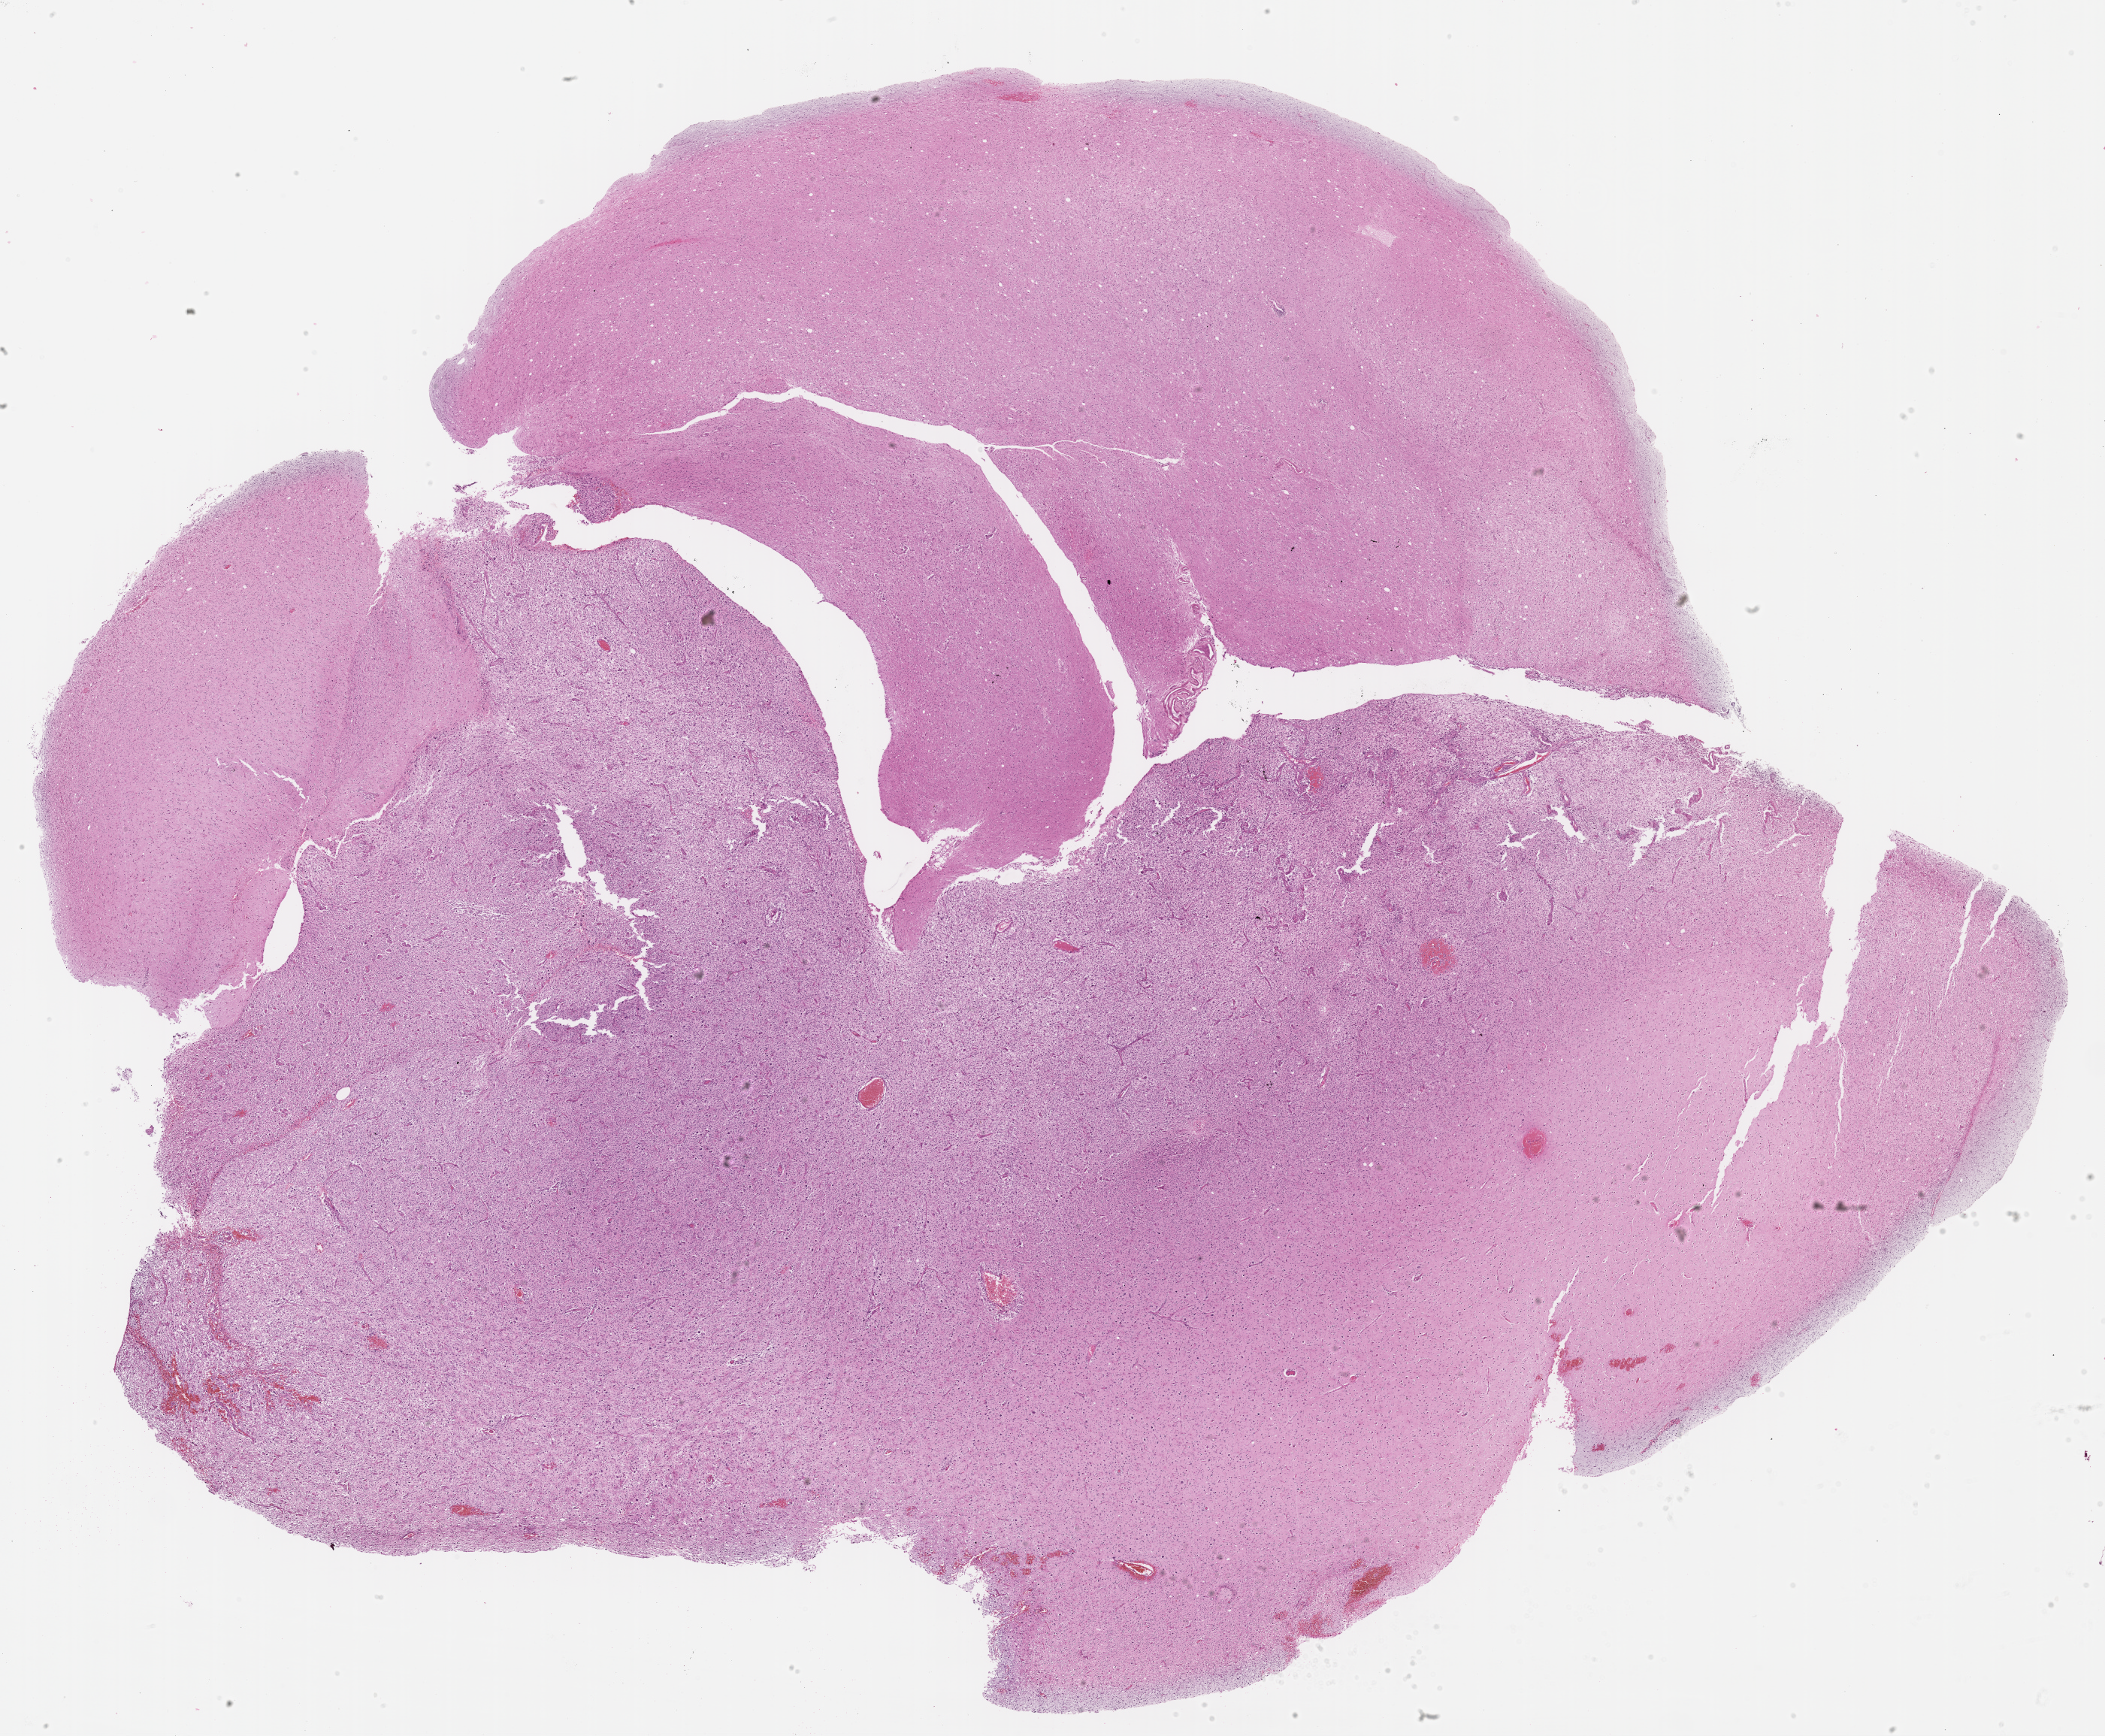
Digitized H&E tissue section (whole slide) — whole scanned area (about 22.7 x 18.7 mm) shown as a low-resolution overview. Formalin-fixed paraffin-embedded (FFPE) diagnostic section. Sample: primary tumour, brain. Male, age 67 years at initial diagnosis.
- pathologic diagnosis: Glioblastoma